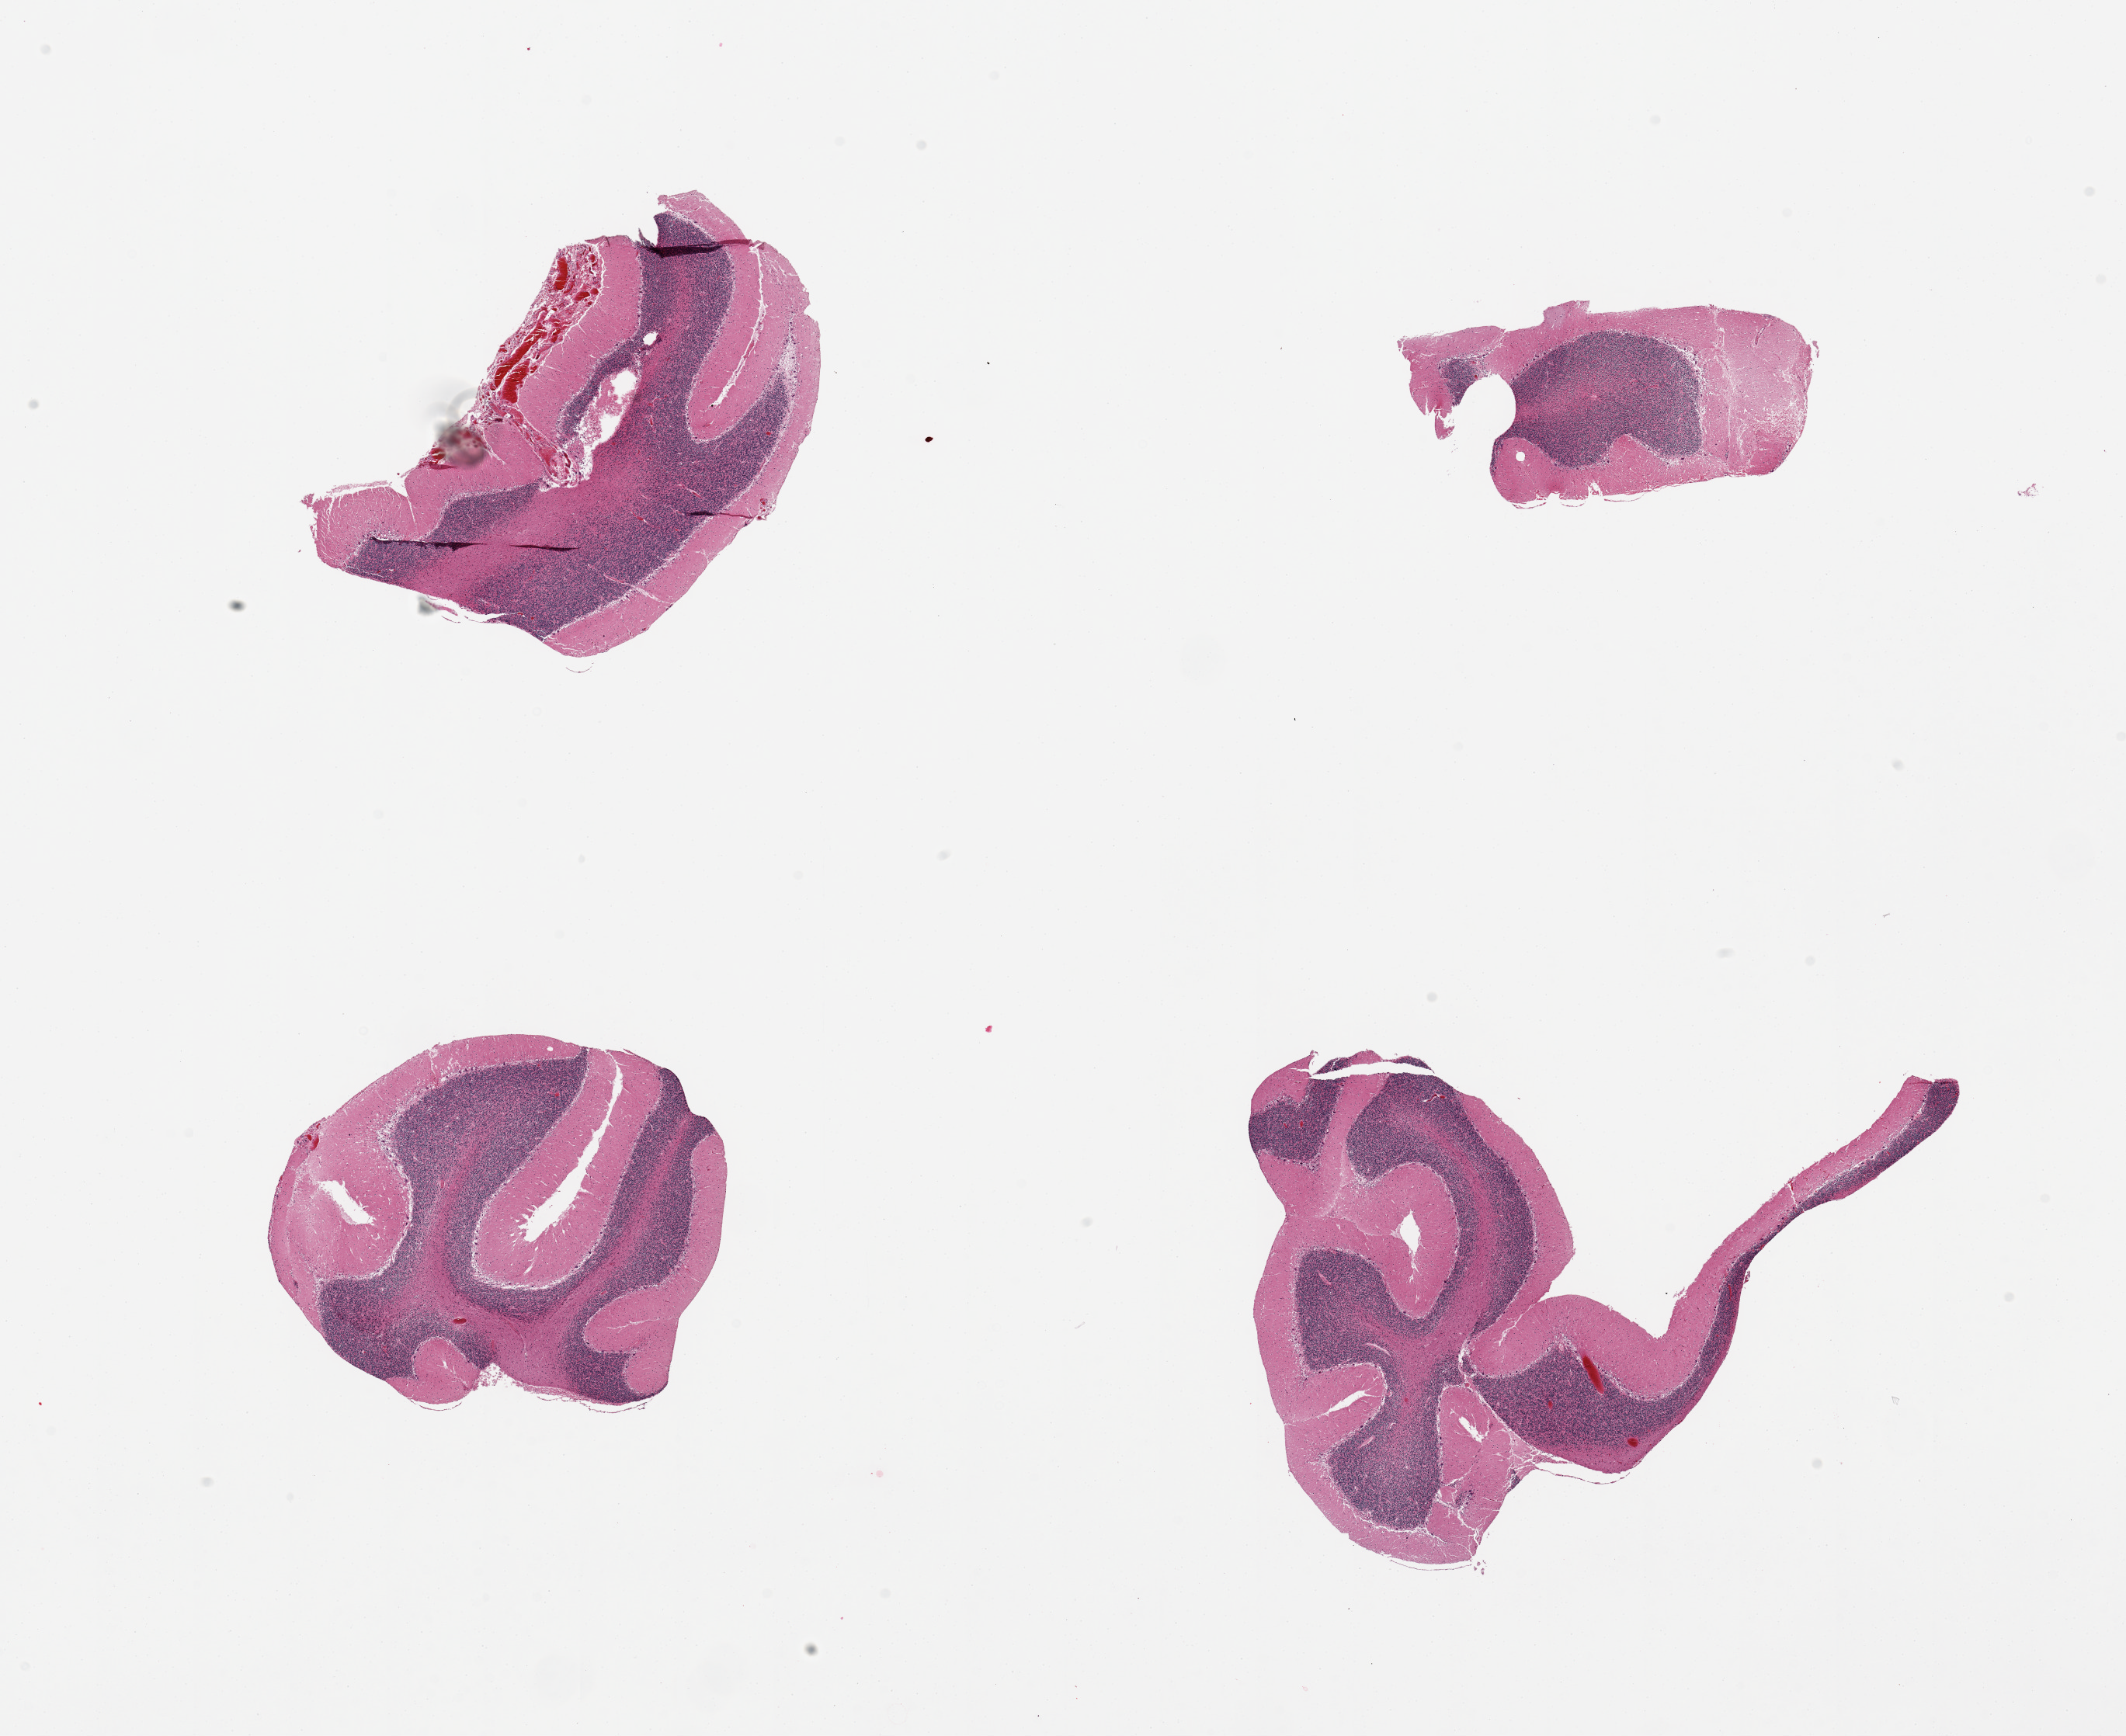
Hematoxylin and eosin (H&E) whole-slide image, shown as a low-resolution overview of the whole scanned area (about 21.7 x 17.7 mm); PAXgene-fixed paraffin-embedded (PFPE) section; sampled site (target tissue): cerebellum; tissue donor sample. Donor sex: male.
- reviewer comment on this tissue sample: 4 pieces, granular layer well defined; Purkinje cells show minimal ischemic damage